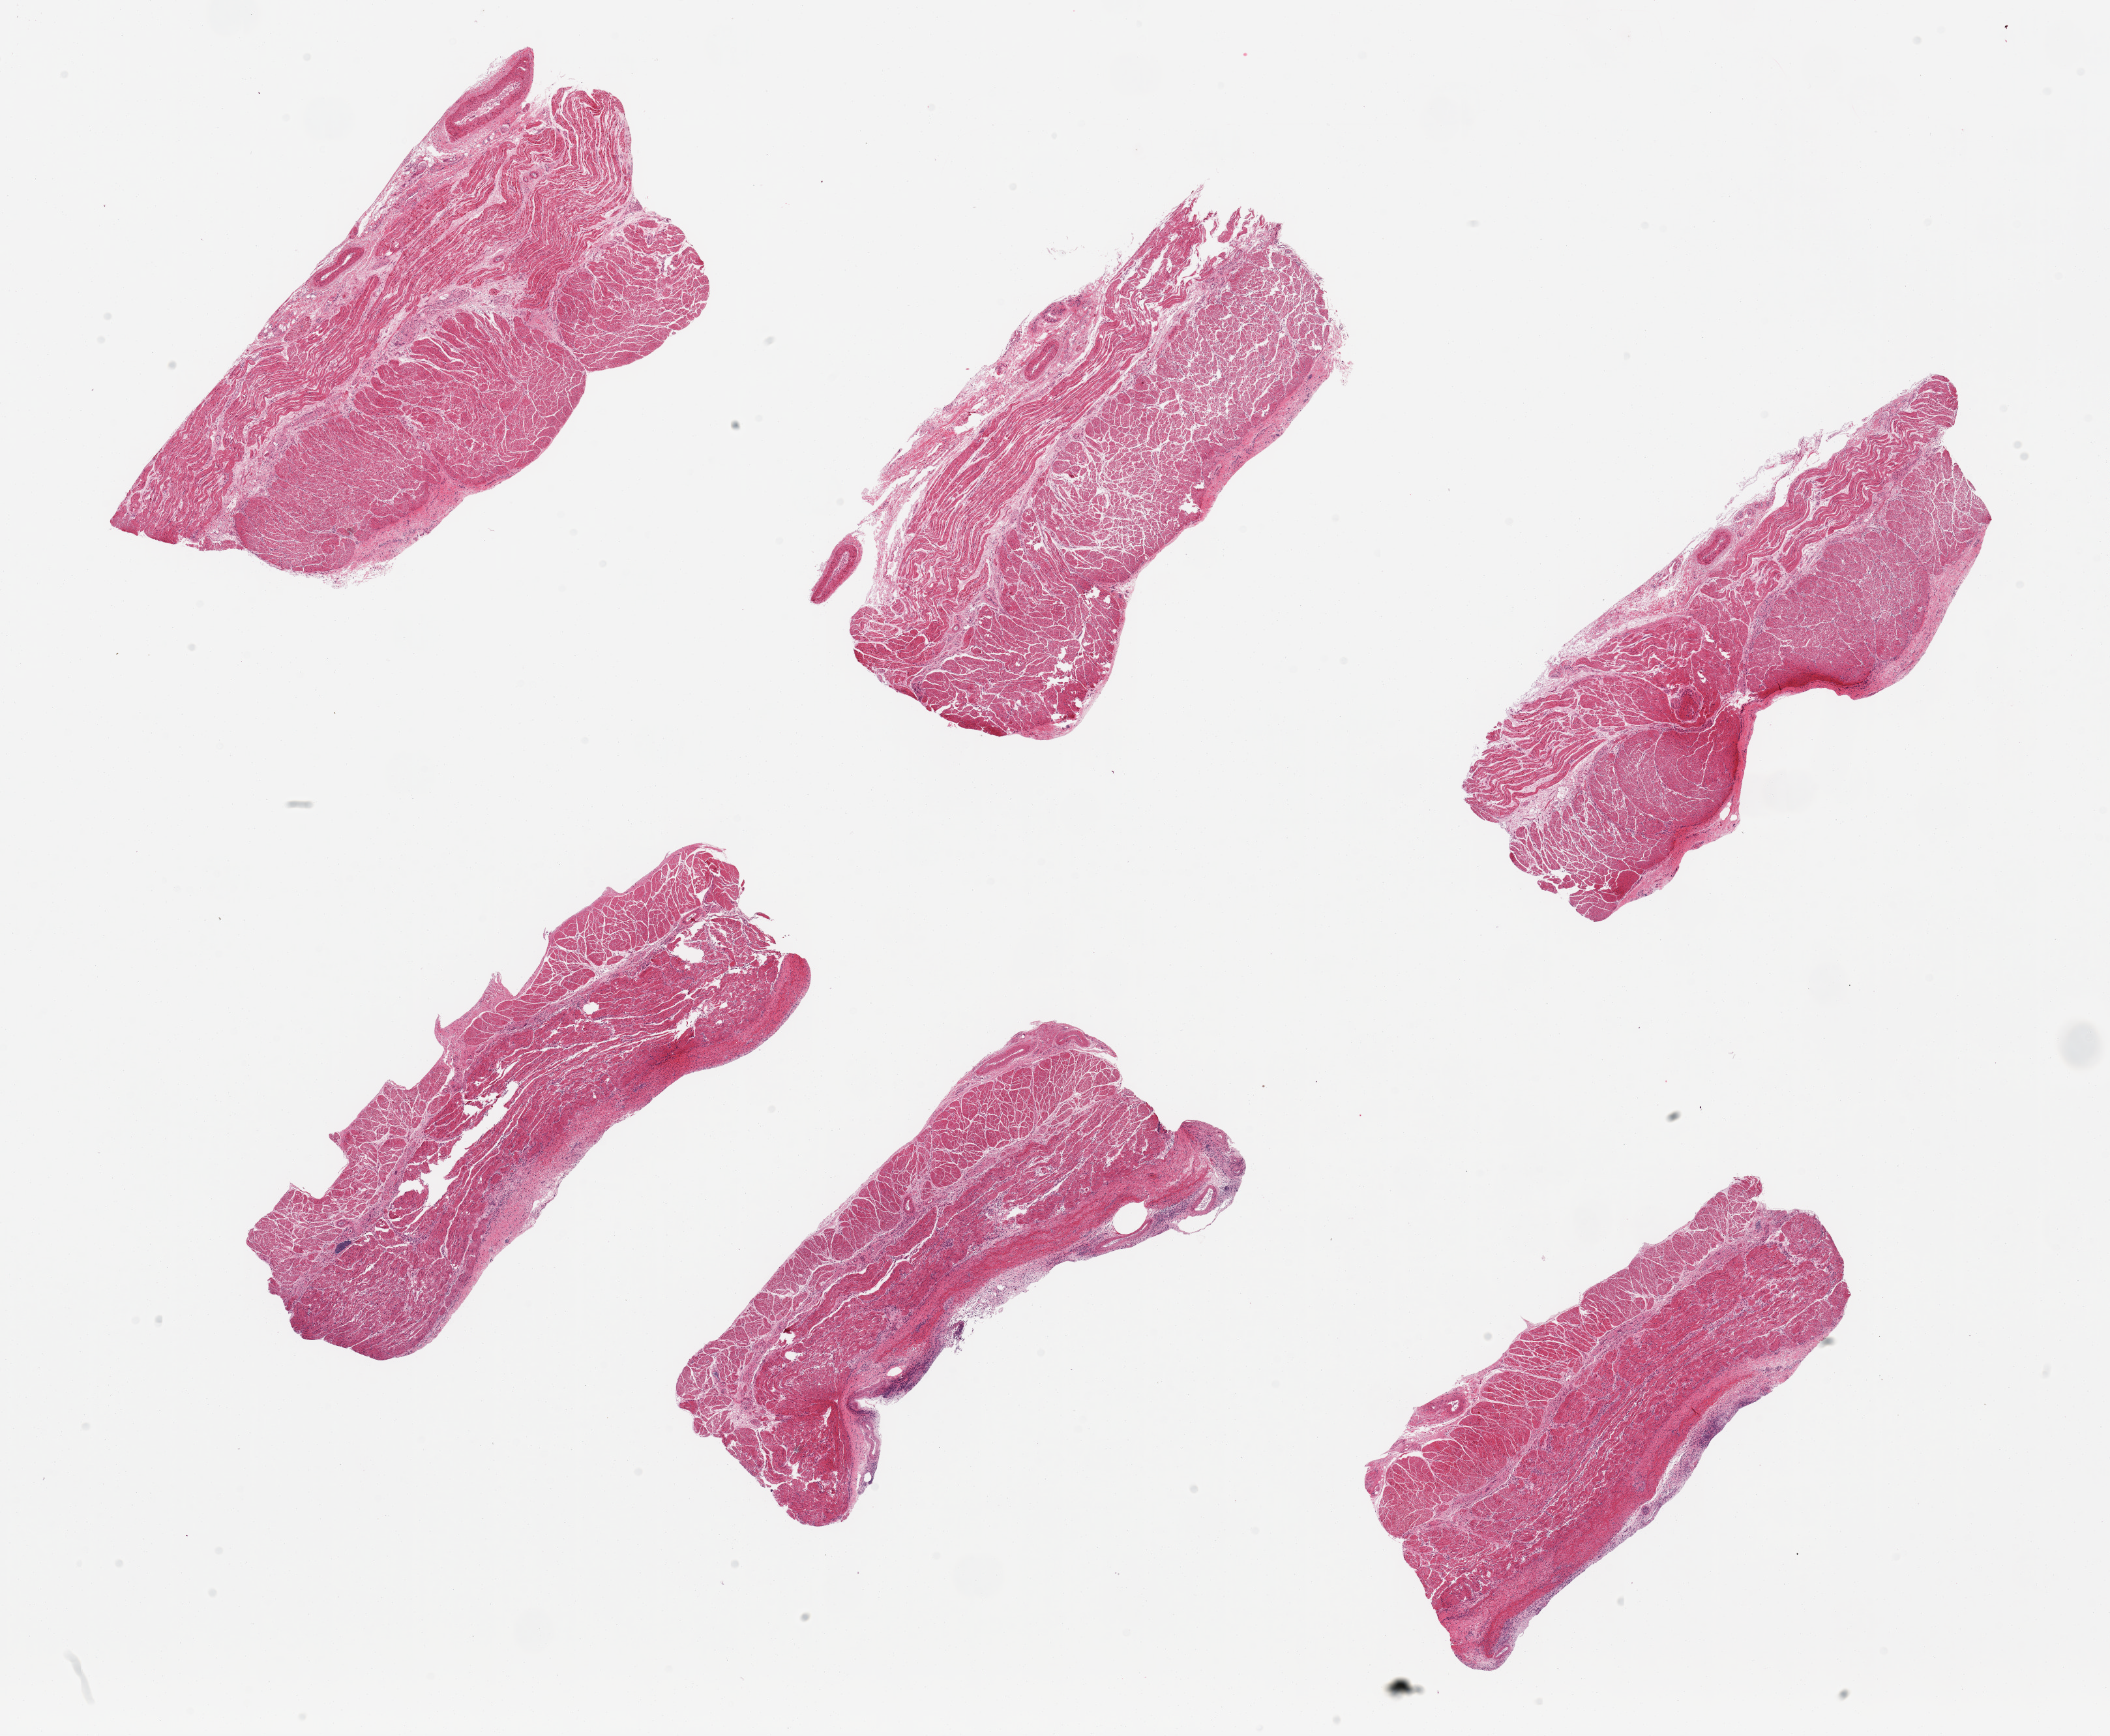
Digitized H&E-stained section, whole scanned area (about 25.6 x 21.1 mm, from a 20x scan) shown as a low-resolution overview, PAXgene-fixed, paraffin-embedded tissue, sampled site (target tissue): gastroesophageal junction, tissue donor sample. Female donor.
• pathologist's review note for this sample: 6 pieces, mainly target muscularis, minute focus of autlyzed mucosa